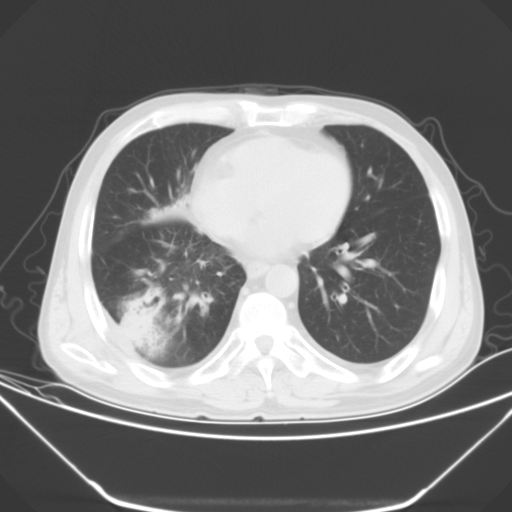
Chest CT, one axial slice. 120 kVp. Lung window (W 1500 / L -600 HU). 5 mm slice thickness. 512 × 512 image matrix, field of view 379 × 379 mm. Male patient, age 54 years. Case-level facts recorded for this patient, not image findings: clinical TNM (as recorded): T2 N1 M0.
Outlined on this slice (rectangle marked by the reading radiologist):
- lung tumour (recorded histology: adenocarcinoma): bounding box <118,287,160,350> (left, top, right, bottom; pixels)